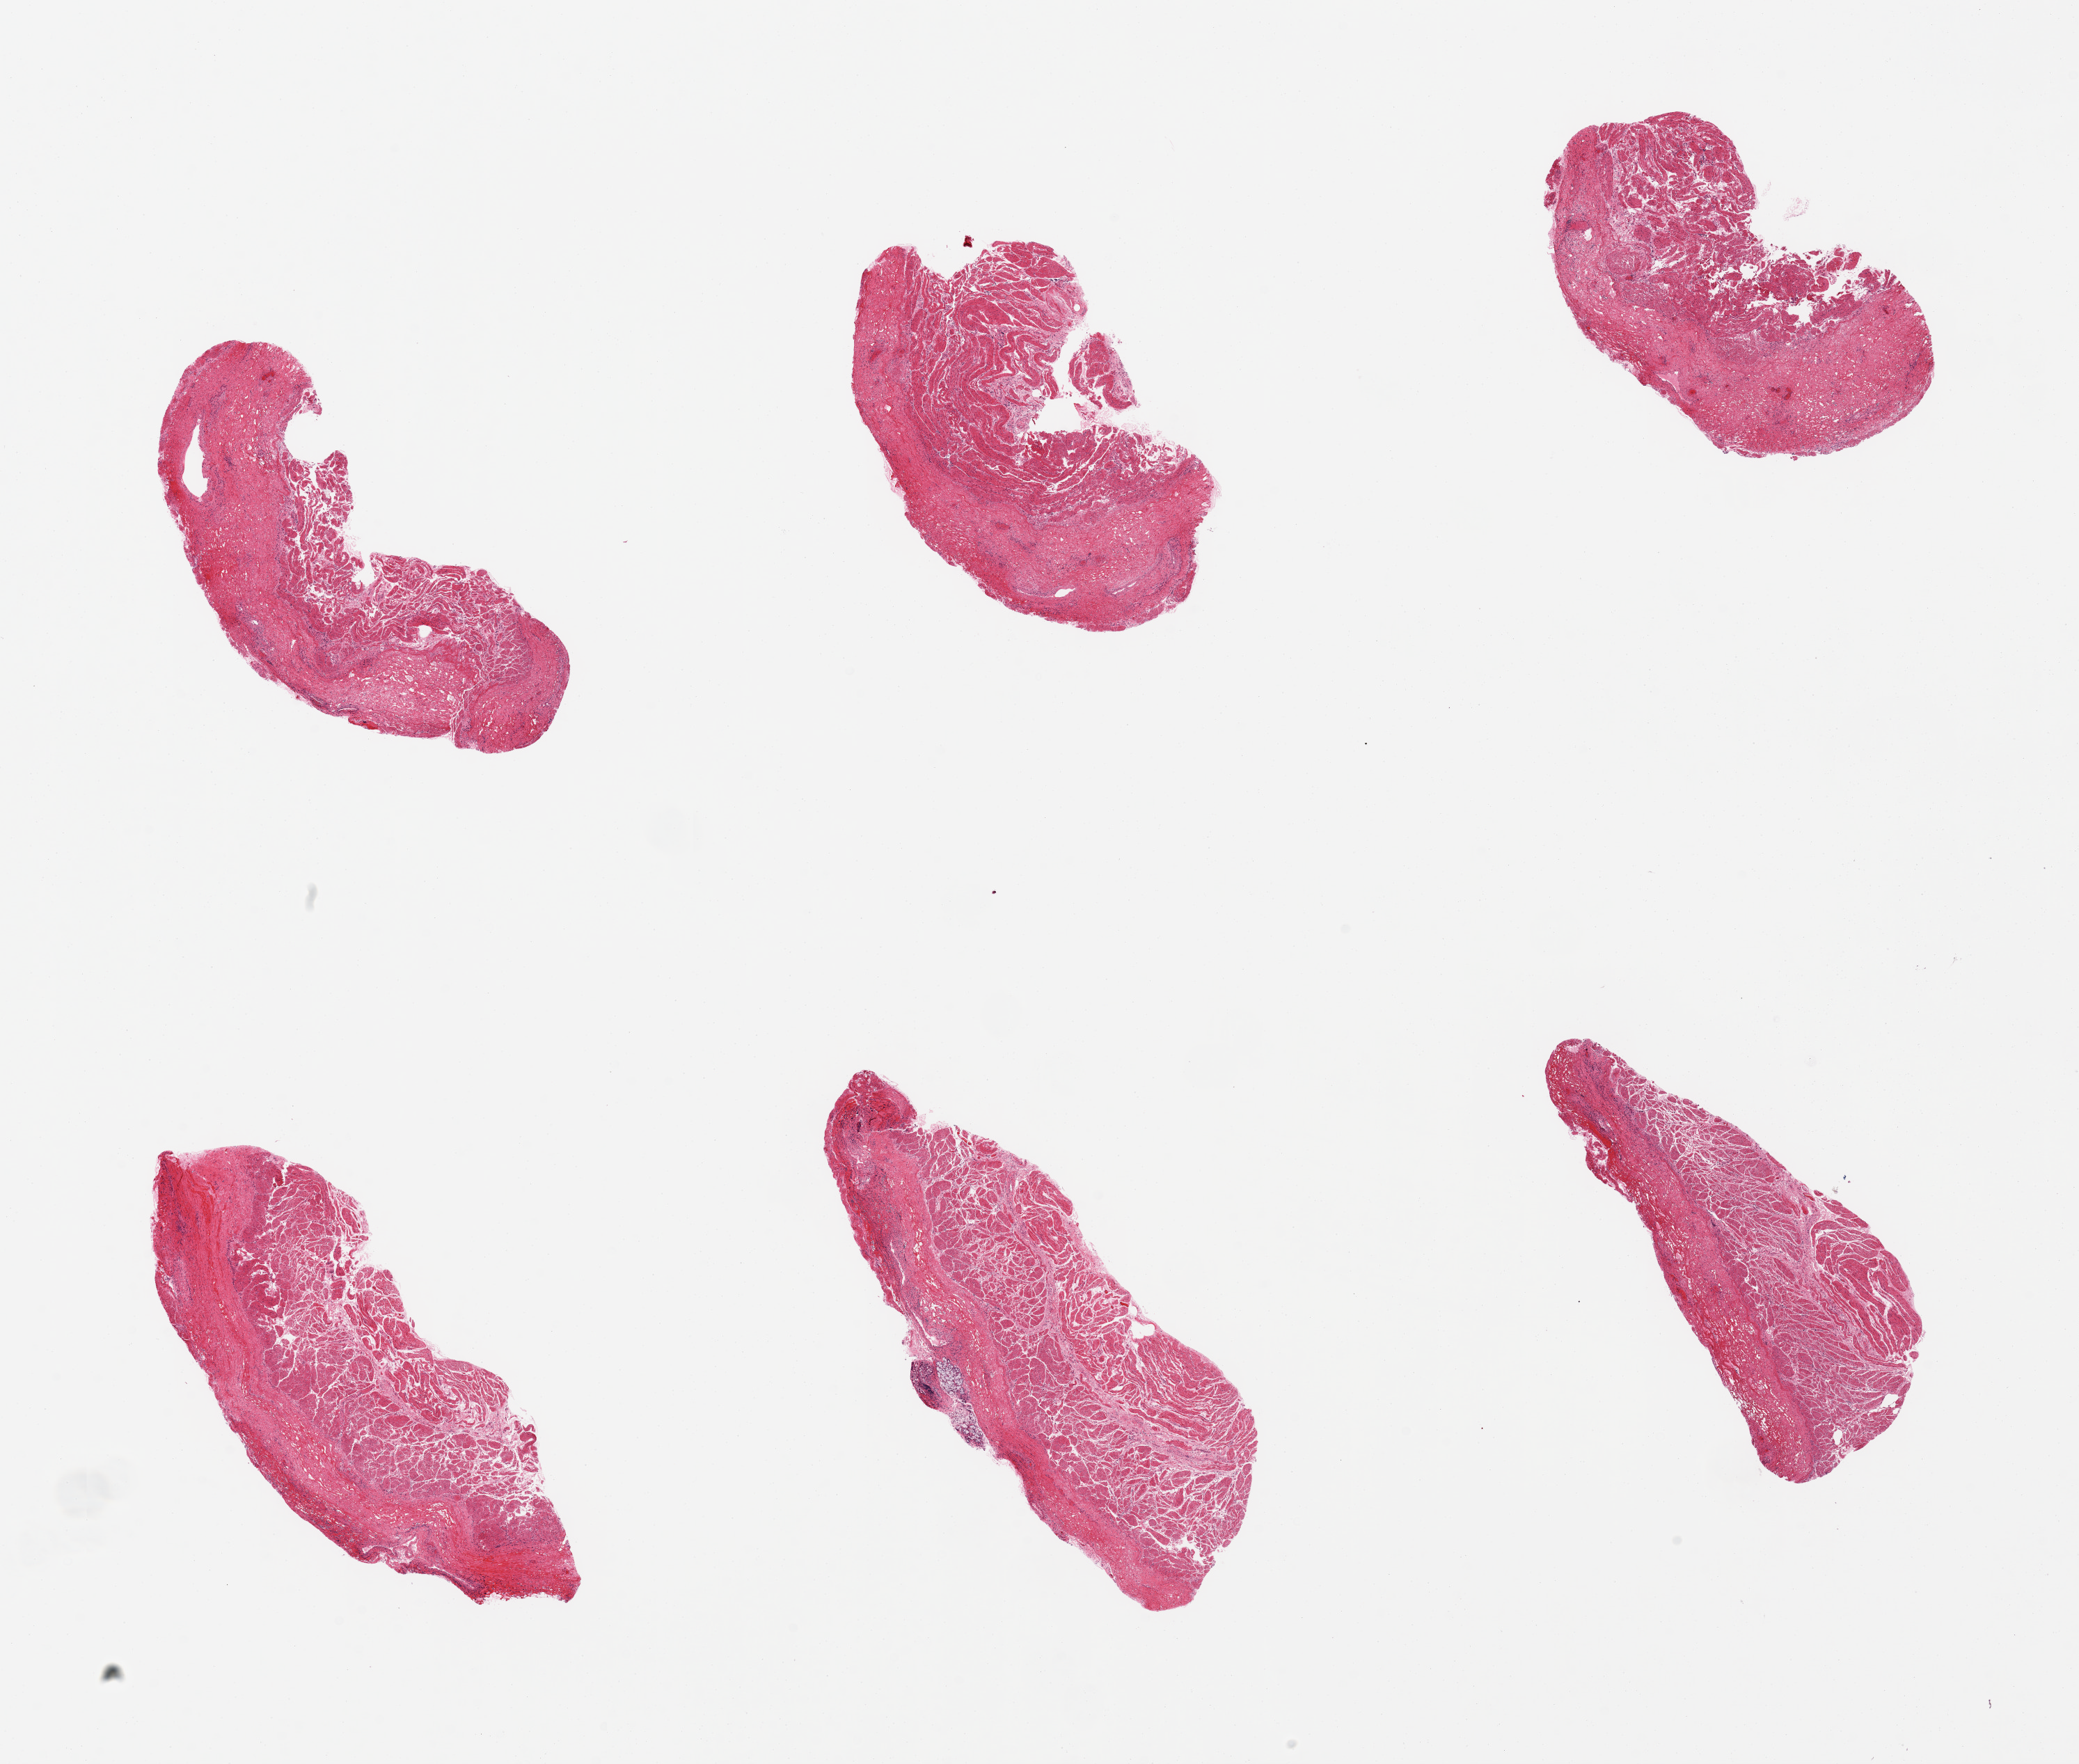
Whole-slide image, H&E stain — low-resolution overview of the scanned area, about 23.6 x 20.0 mm. PAXgene-fixed, paraffin-embedded tissue. Sampled site (target tissue): esophageal muscle. Tissue donor sample. Donor: female.
- pathologist's review note for this sample: 6 pieces, all muscularis